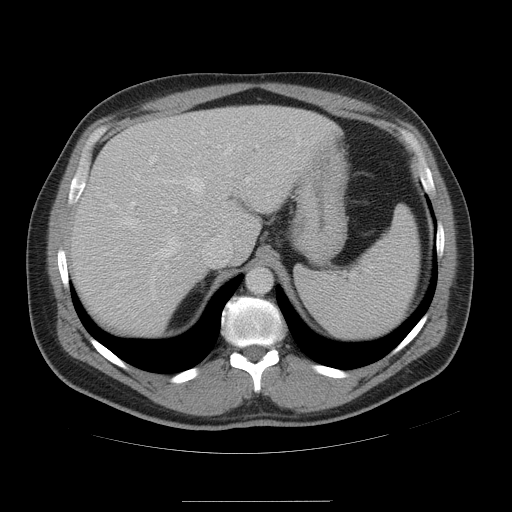
Contrast-enhanced abdominal CT, one axial slice. Position 38 of 54 along the scan axis. 120 kVp. Intravenous contrast given. Soft-tissue window (W 400 / L 40 HU). 5 mm slice thickness. 512 × 512 image matrix, field of view 436 × 436 mm. Male patient, age 40 years. Case-level facts recorded for this patient, not image findings: diagnosis: colorectal cancer liver metastases, imaged before liver resection; multiple liver metastases: no; largest metastasis: 15 cm; disease in both lobes: no.
Structures marked on this image (expert manual segmentation):
- hepatic veins: bounding box <110,152,230,299> (left, top, right, bottom; pixels)
- liver: <70,106,340,337>
- planned liver remnant (the part of the liver to remain after resection): <179,106,340,273>
- portal vein (with intrahepatic branches): <132,134,246,213>